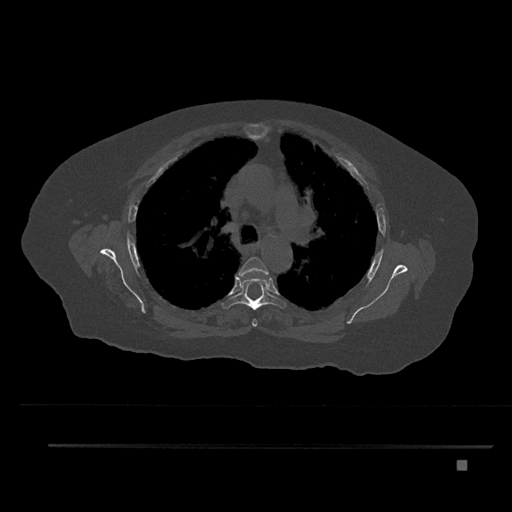
CT including the spine, one axial slice; slice 577 of 797 in the series (ordered by position); reconstruction kernel Br40s/3; bone window (W 1800 / L 400 HU); 0.5 mm slice thickness; 512 × 512 image matrix, field of view 437 × 437 mm. Patient: female, 76 years. Case-level facts recorded for this patient, not image findings: primary cancer: lung; vertebrae with lytic lesions (as recorded): T11, L3.
Annotated regions visible in this slice (semi-automatic segmentation, software-assisted and operator-edited):
- T4 vertebra: box from (x=237, y=257) to (x=269, y=327) px
- T5 vertebra: (x=222, y=278)–(x=286, y=310)